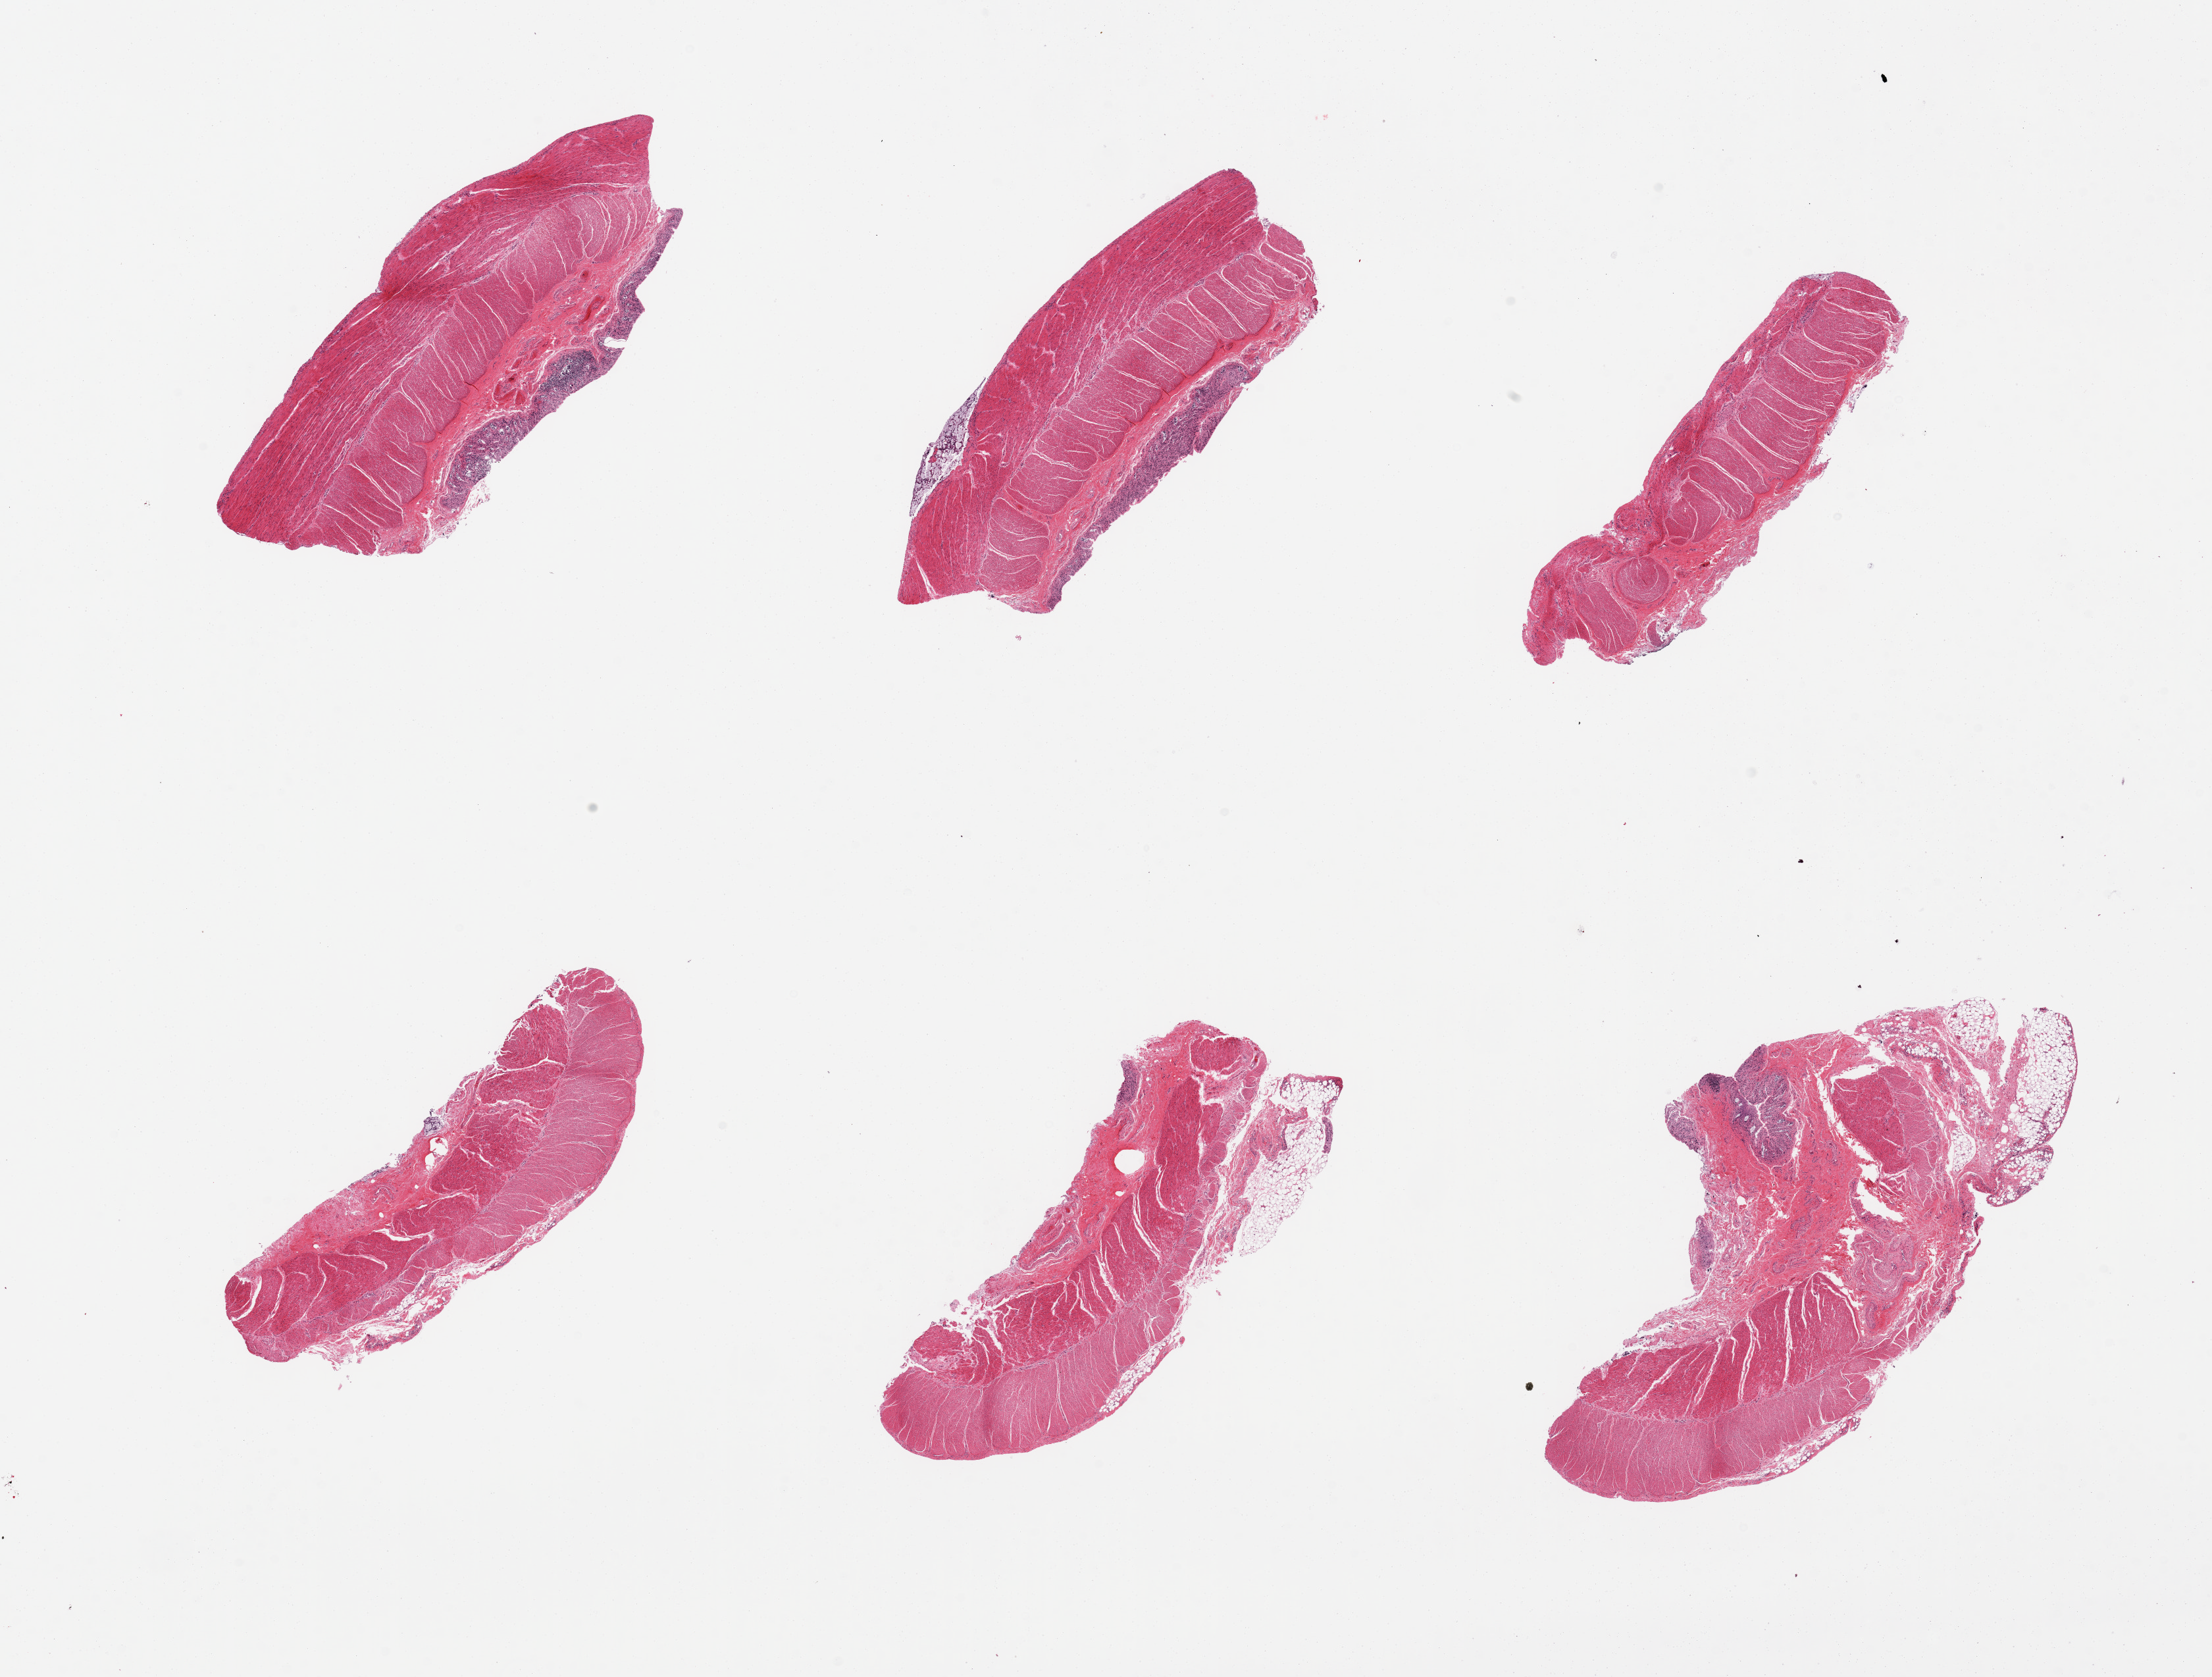
Digitized haematoxylin and eosin-stained section, brightfield — a low-resolution overview of the entire scanned area, about 26.6 x 20.2 mm (slide scanned at 20x), PAXgene-fixed, paraffin-embedded tissue, section of sigmoid colon (target tissue), donor tissue sample.
Pathologist's review note for this sample: 6 pieces, ~10% adherent completely autolyzed mucosa.